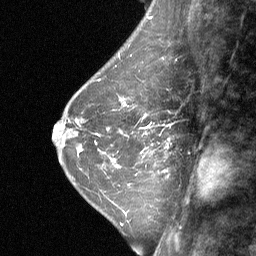
Breast MRI (dynamic contrast-enhanced), one sagittal slice; slice 21 of 64 in the series (ordered by position); dynamic contrast-enhanced study with each time point stored as its own series, time point 2 of 3 at this slice position (early post-contrast, ordered by acquisition time); 1.5 T; TE 4.8 ms, TR 27 ms; 256 × 256 image matrix, field of view 180 × 180 mm. Patient: female, 42 years. From the clinical record (not read from this slice): setting: breast cancer imaged before/during neoadjuvant chemotherapy; receptor status: triple-negative.
Annotated regions visible in this slice (semi-automatically segmented with operator editing):
- analysis volume of interest (the breast-tissue region the enhancement analysis was run in; not a lesion): bounding box [x1, y1, x2, y2] px = [124, 96, 172, 161]
- tumour enhancement mask (voxels above the 90 % enhancement threshold inside the analysis volume of interest): [145, 125, 149, 134]